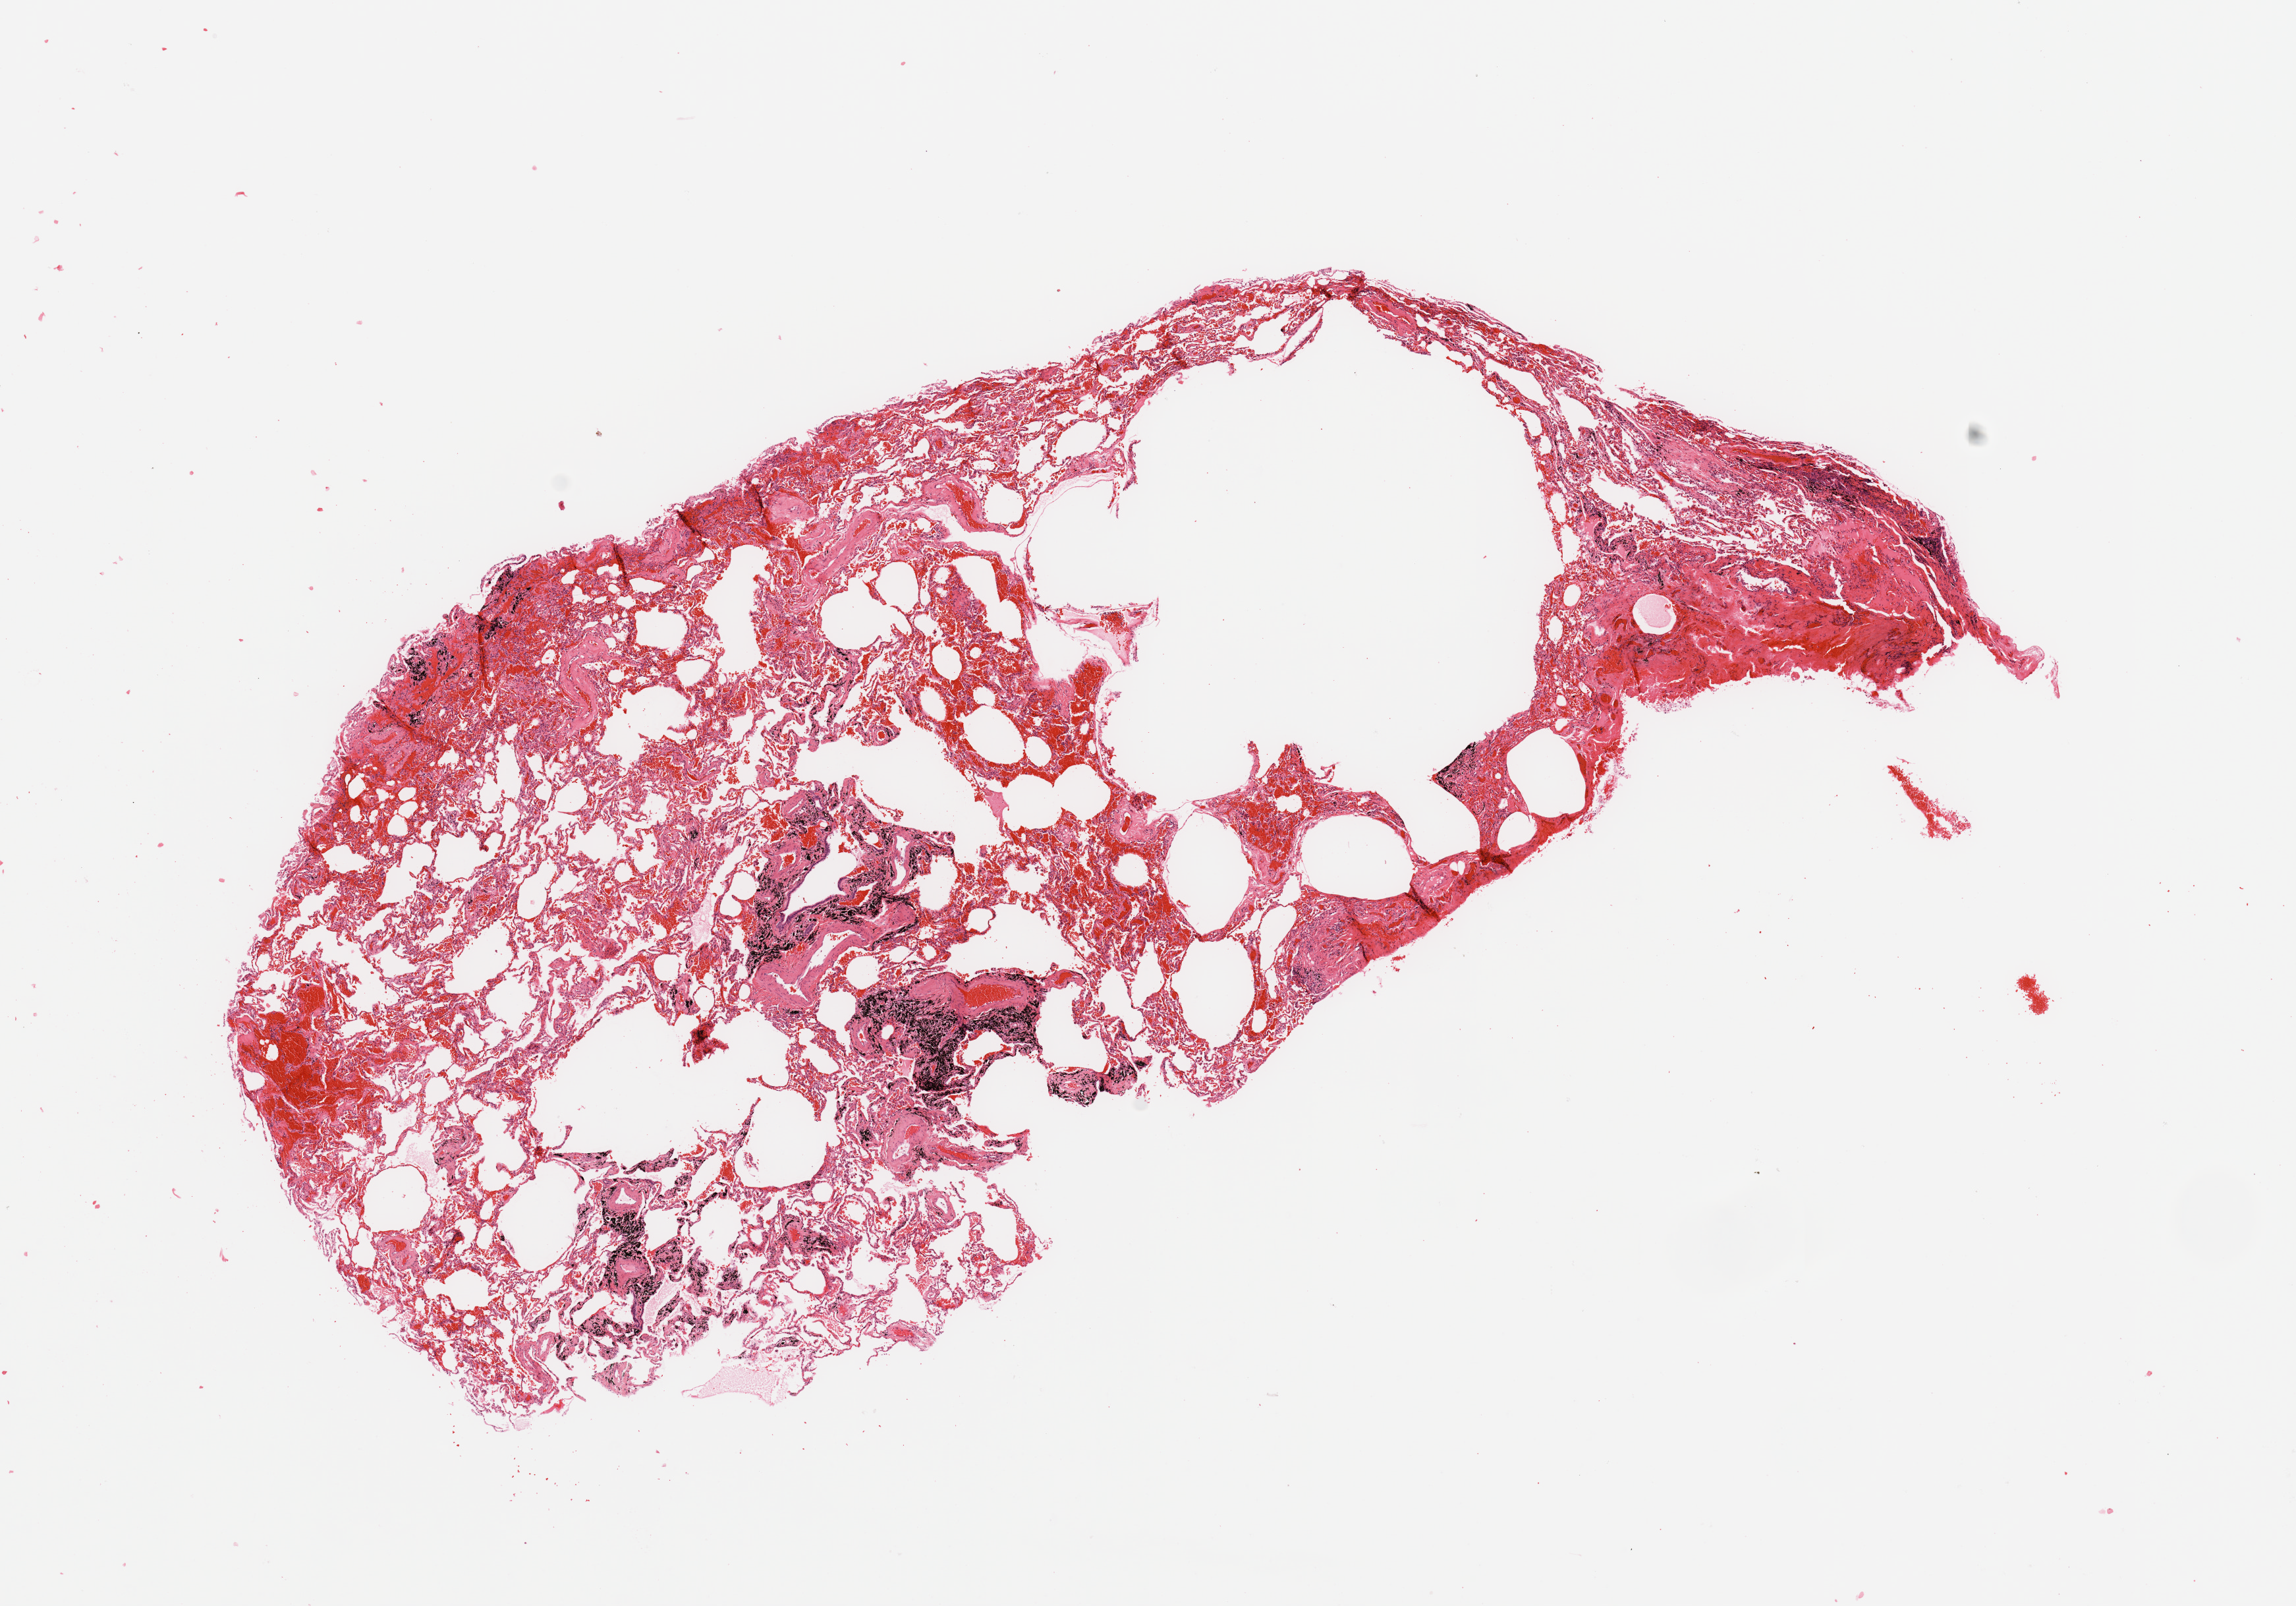
Whole-slide histology image, Hematoxylin and eosin (H&E) stained, a low-resolution overview of the entire scanned area, about 13.8 x 9.6 mm. Normal (non-tumour) tissue sample, lung. Patient: male, age 72 years.
This section: normal (non-tumour) tissue from the same patient. Patient diagnosis: Adenocarcinoma, NOS.